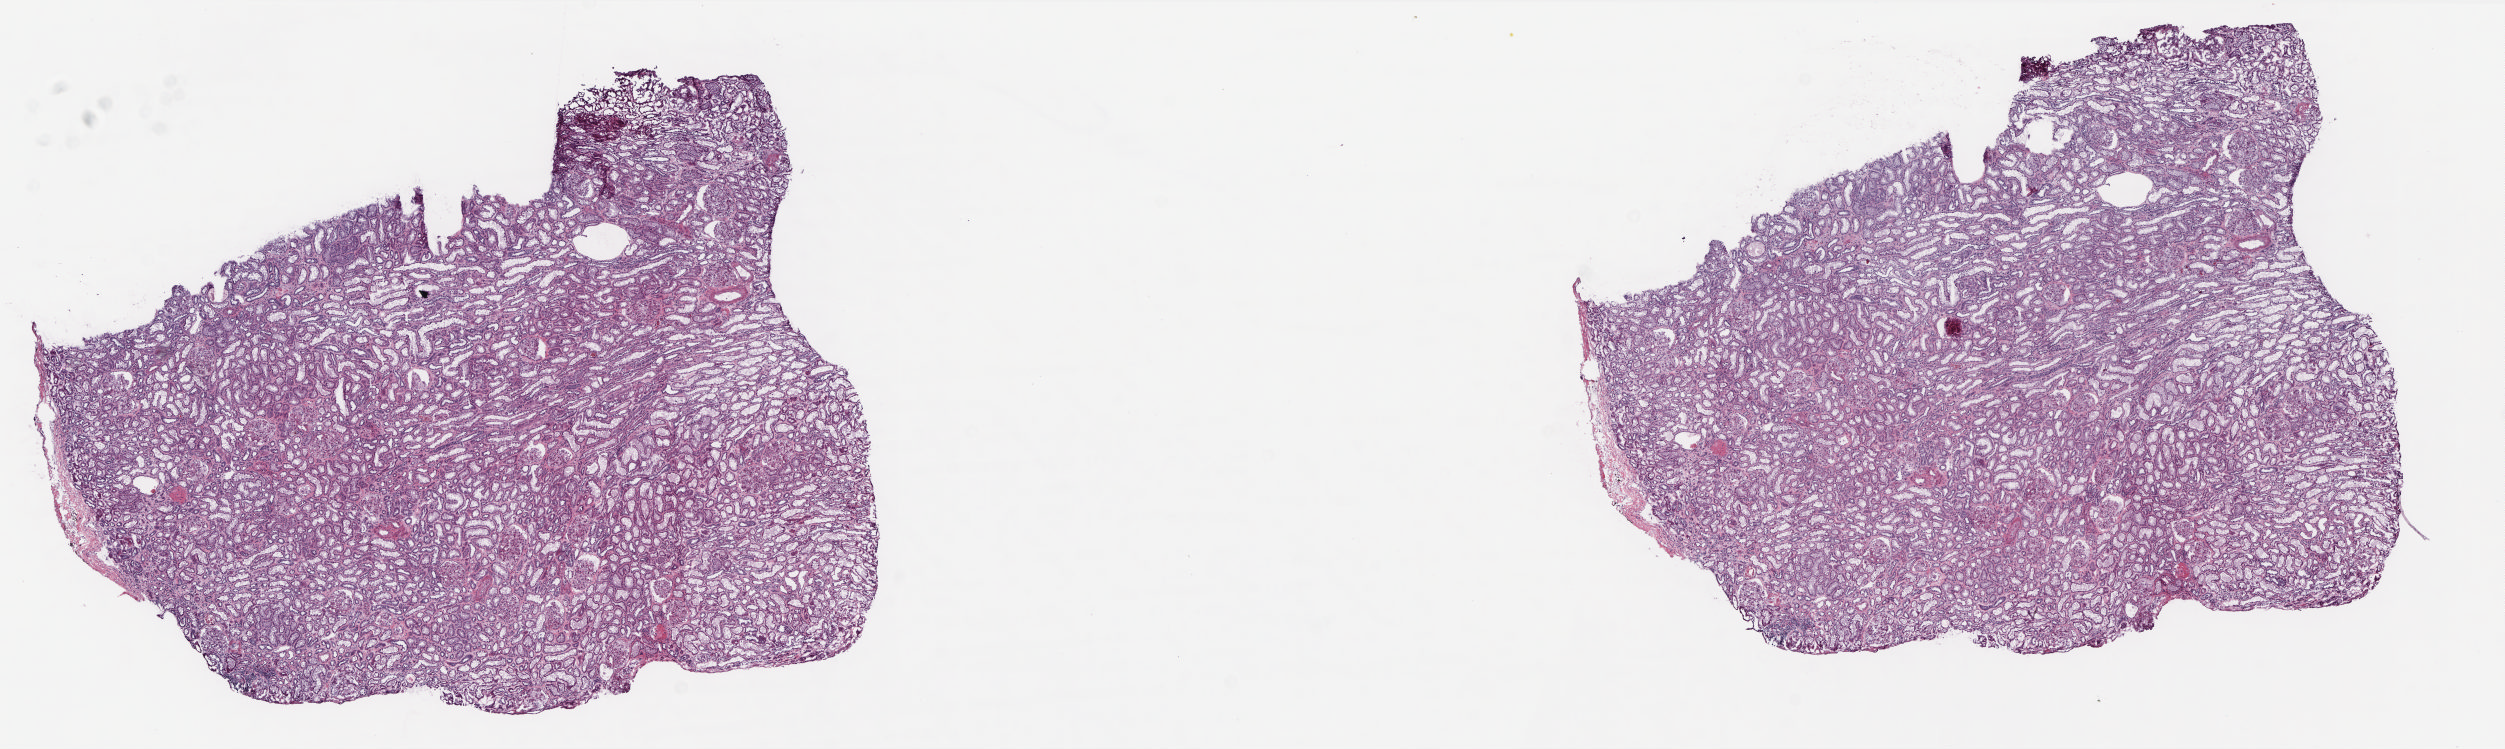
Digitized Hematoxylin and eosin (H&E) stained tissue section (whole slide), low-resolution overview of the scanned area, about 20.2 x 6.0 mm; frozen section from the top of the tissue portion; sample: solid tissue normal (non-tumour tissue), kidney. Patient: female, age at initial diagnosis 76 years. Composition of this section per pathologist review: tumour cells 0%, tumour nuclei 0%, normal cells 80%, stromal cells 20%, necrosis 0%. Inflammatory infiltration, as recorded: lymphocyte infiltration 3%, monocyte infiltration 1%, neutrophil infiltration 2%.
- this section: solid tissue normal (non-tumour) sample from the same patient
- patient diagnosis: Renal cell carcinoma, NOS